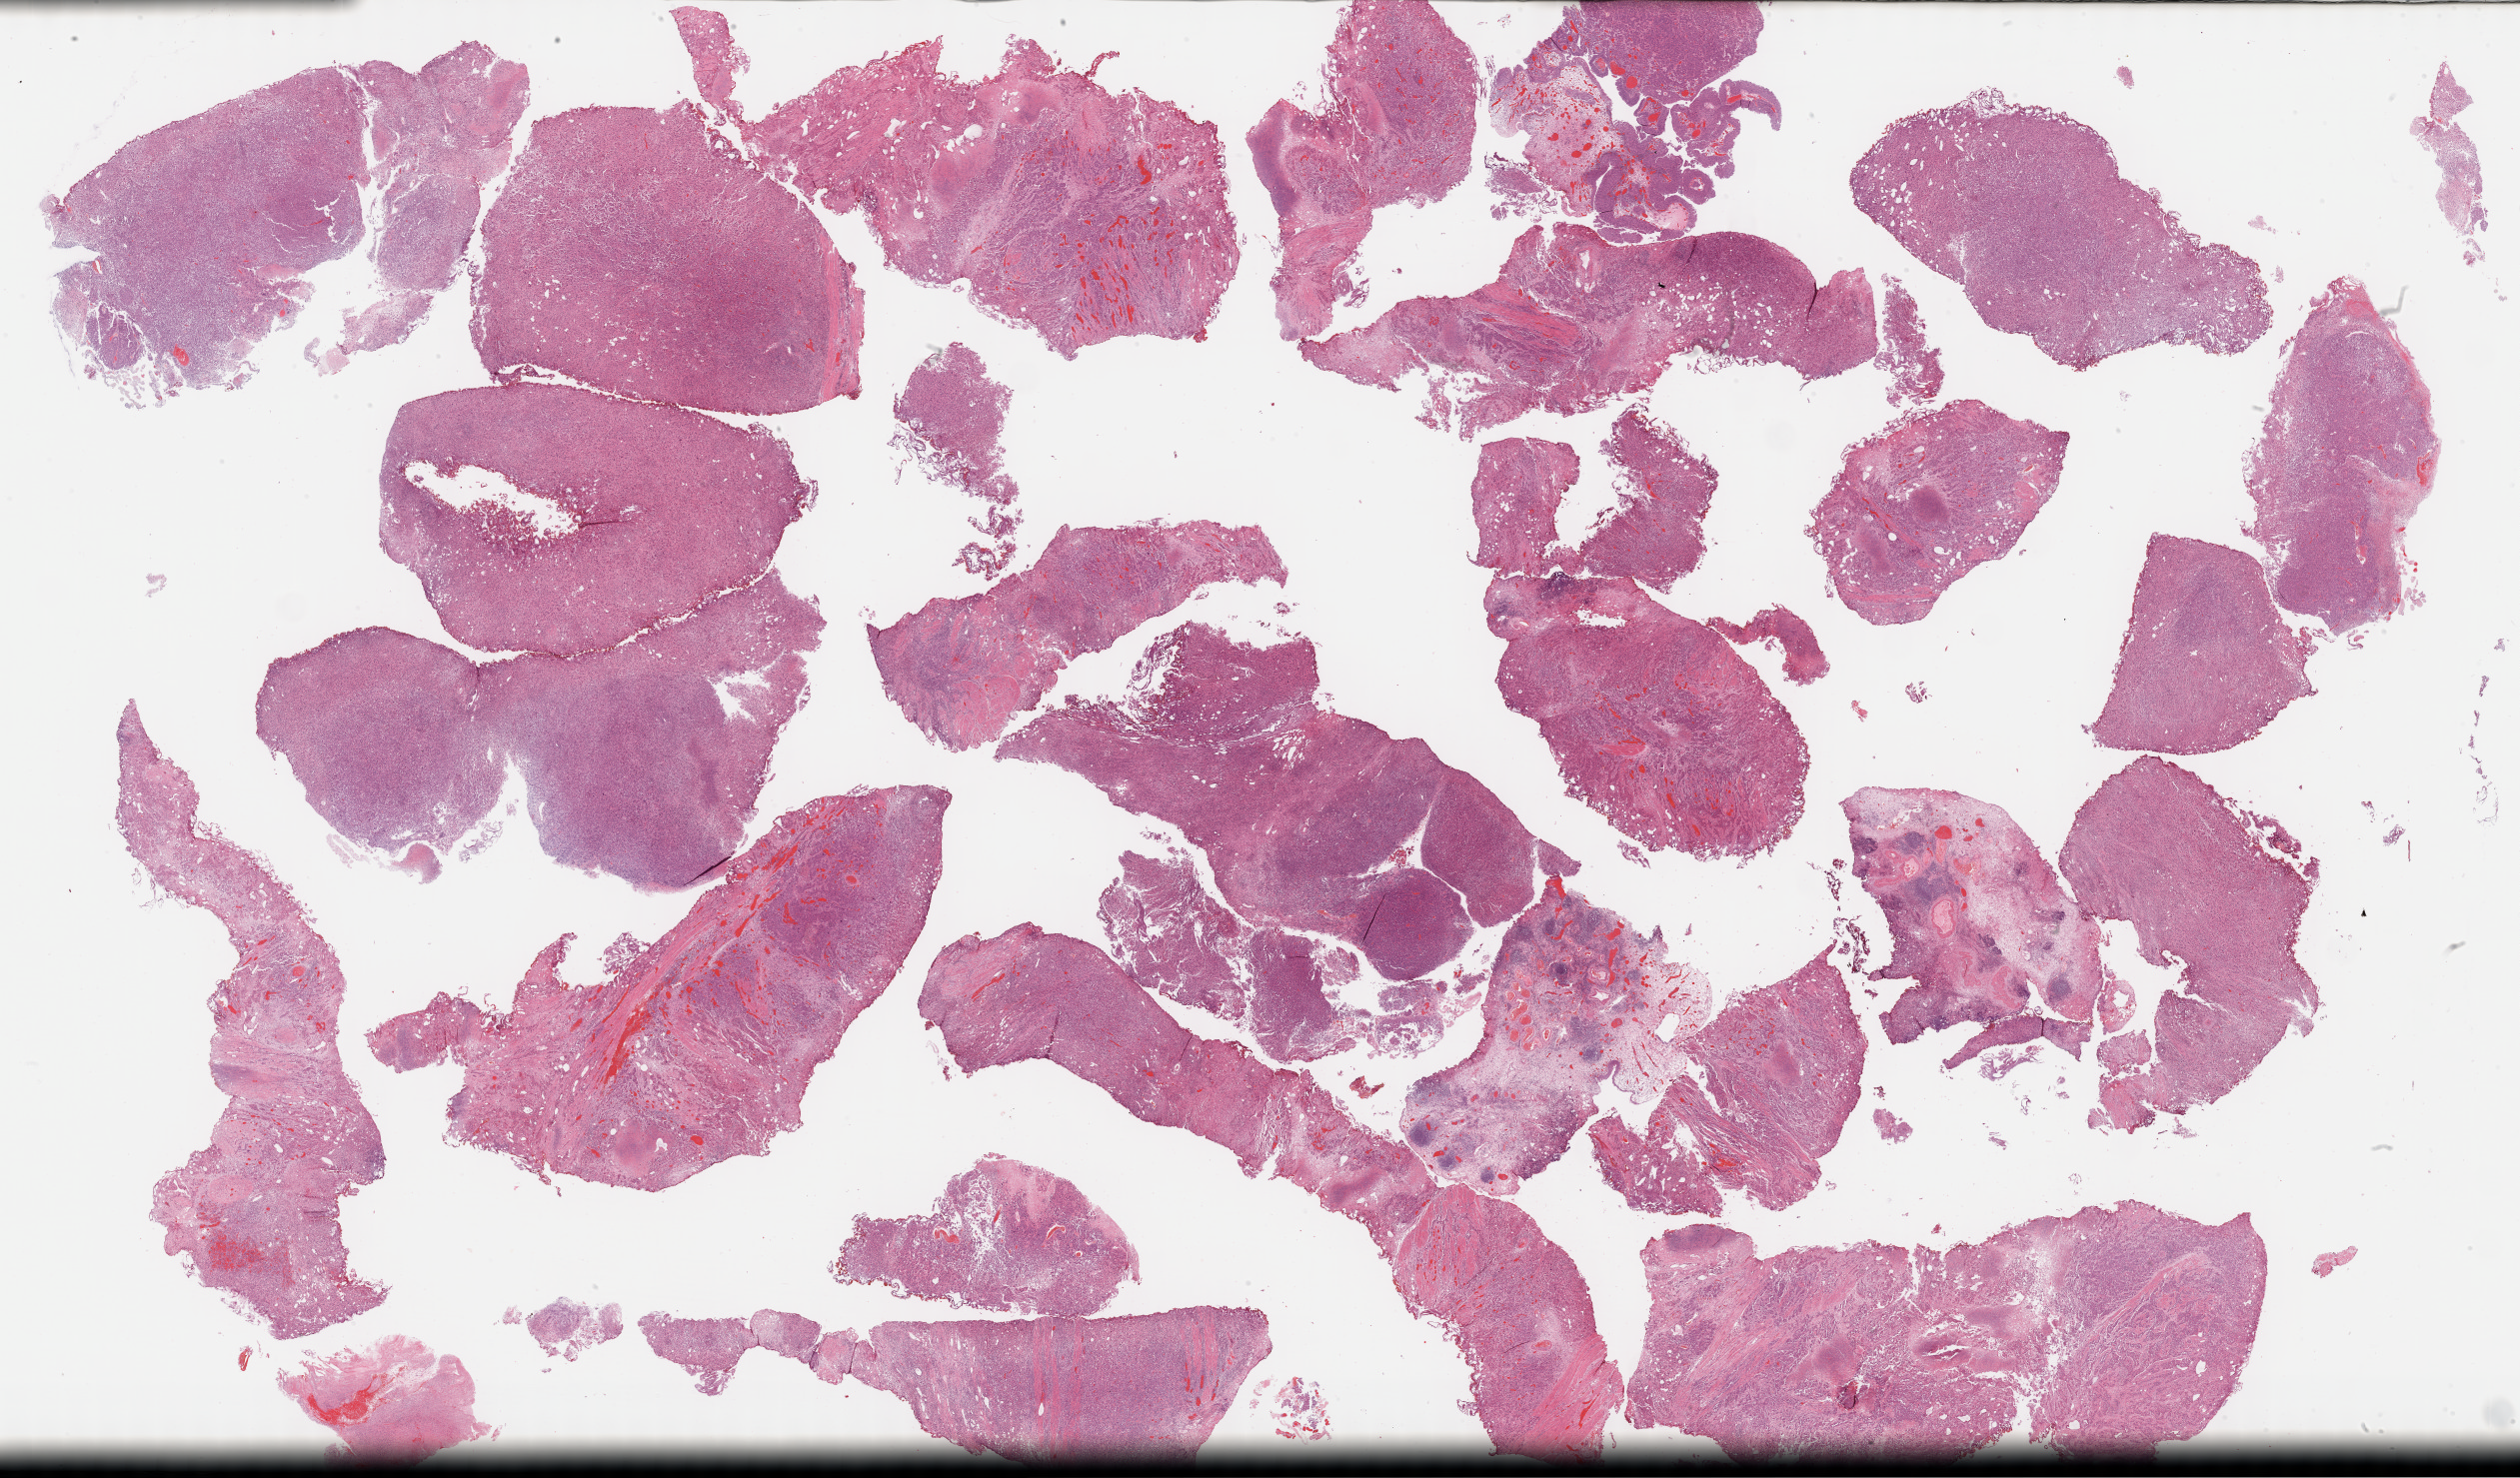
Digitized H&E tissue section (whole slide) — whole scanned area (about 40.8 x 23.9 mm) shown as a low-resolution overview; formalin-fixed paraffin-embedded (FFPE) diagnostic section; primary tumour sample from the bladder. Male patient; age at initial diagnosis 74 years. Histologic grade: high grade.
AJCC pathologic stage: II (6th edition). Histologic diagnosis: Transitional cell carcinoma.